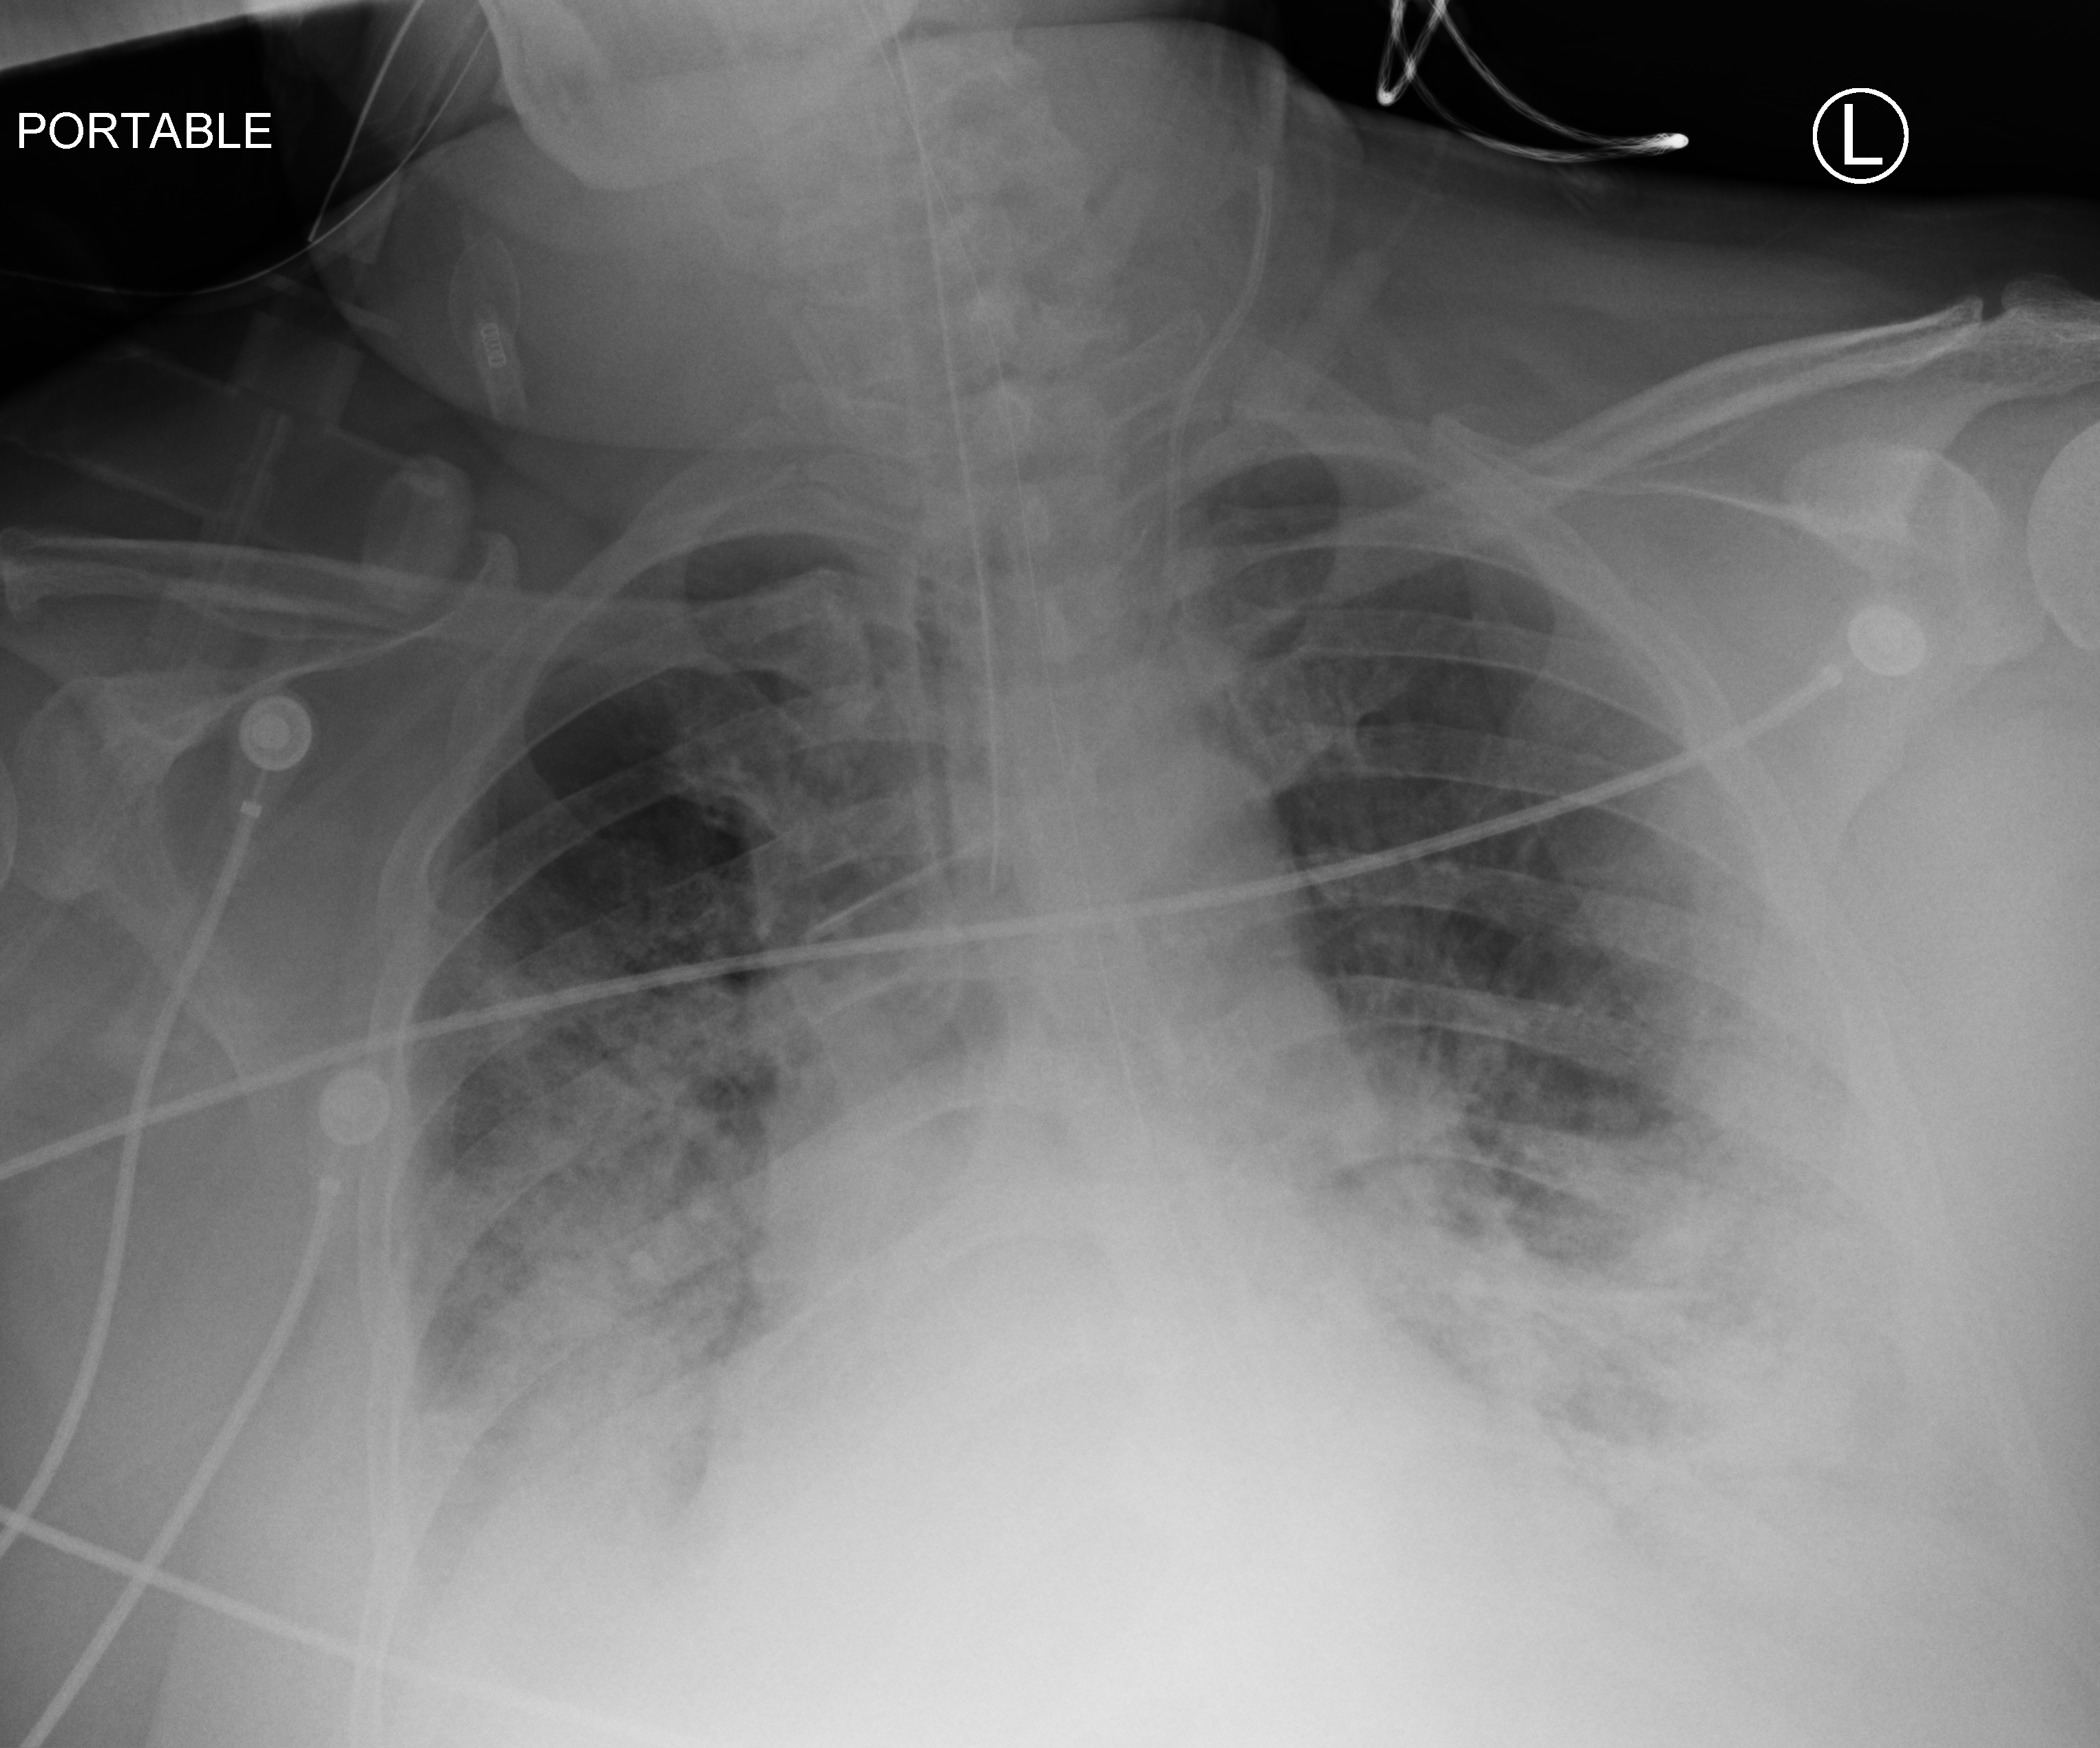
Portable chest radiograph. Adult patient hospitalised with COVID-19, age 18–59 years.
Admission-level facts for this patient (not findings on this image; timing relative to this image not recorded): mechanically ventilated during this hospital stay: yes; length of hospital stay: 13 days.